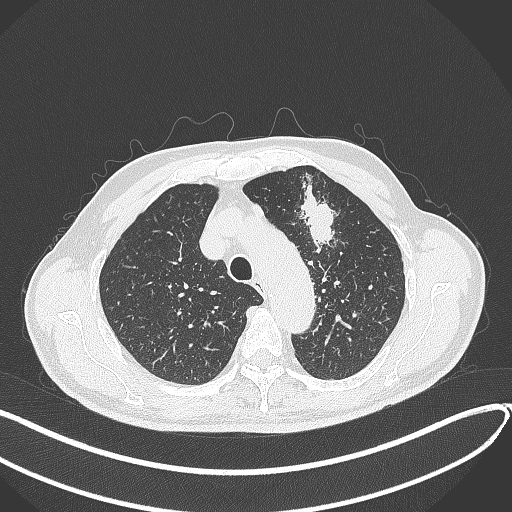
Chest CT, one axial slice; slice 322 of 459 in the series (ordered by position); reconstruction kernel B70f; 120 kVp; lung window (W 1500 / L -600 HU); 512 × 512 image matrix, field of view 400 × 400 mm. Patient: male, 74 years. Case-level facts recorded for this patient, not image findings: clinical TNM (as recorded): T2b N0 M1c.
Outlined on this slice (bounding box drawn by a radiologist):
- lung tumour (recorded histology: adenocarcinoma): box from (x=296, y=180) to (x=345, y=257) px